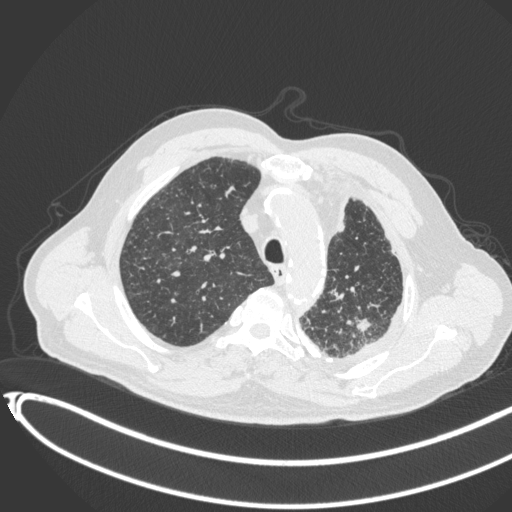
Chest CT, one axial slice. Slice 334 of 451 in the series (ordered by position). Reconstruction kernel B31f. 120 kVp. Lung window (W 1500 / L -600 HU). 512 × 512 image matrix, field of view 400 × 400 mm. Male patient, age 78 years. From the clinical record (not read from this slice): clinical TNM (as recorded): T1c N0 M1.
Annotated regions visible in this slice (bounding box drawn by a radiologist):
- lung tumour (recorded histology: adenocarcinoma): bounding box (x1, y1, x2, y2) in pixels: (348, 312, 373, 336)